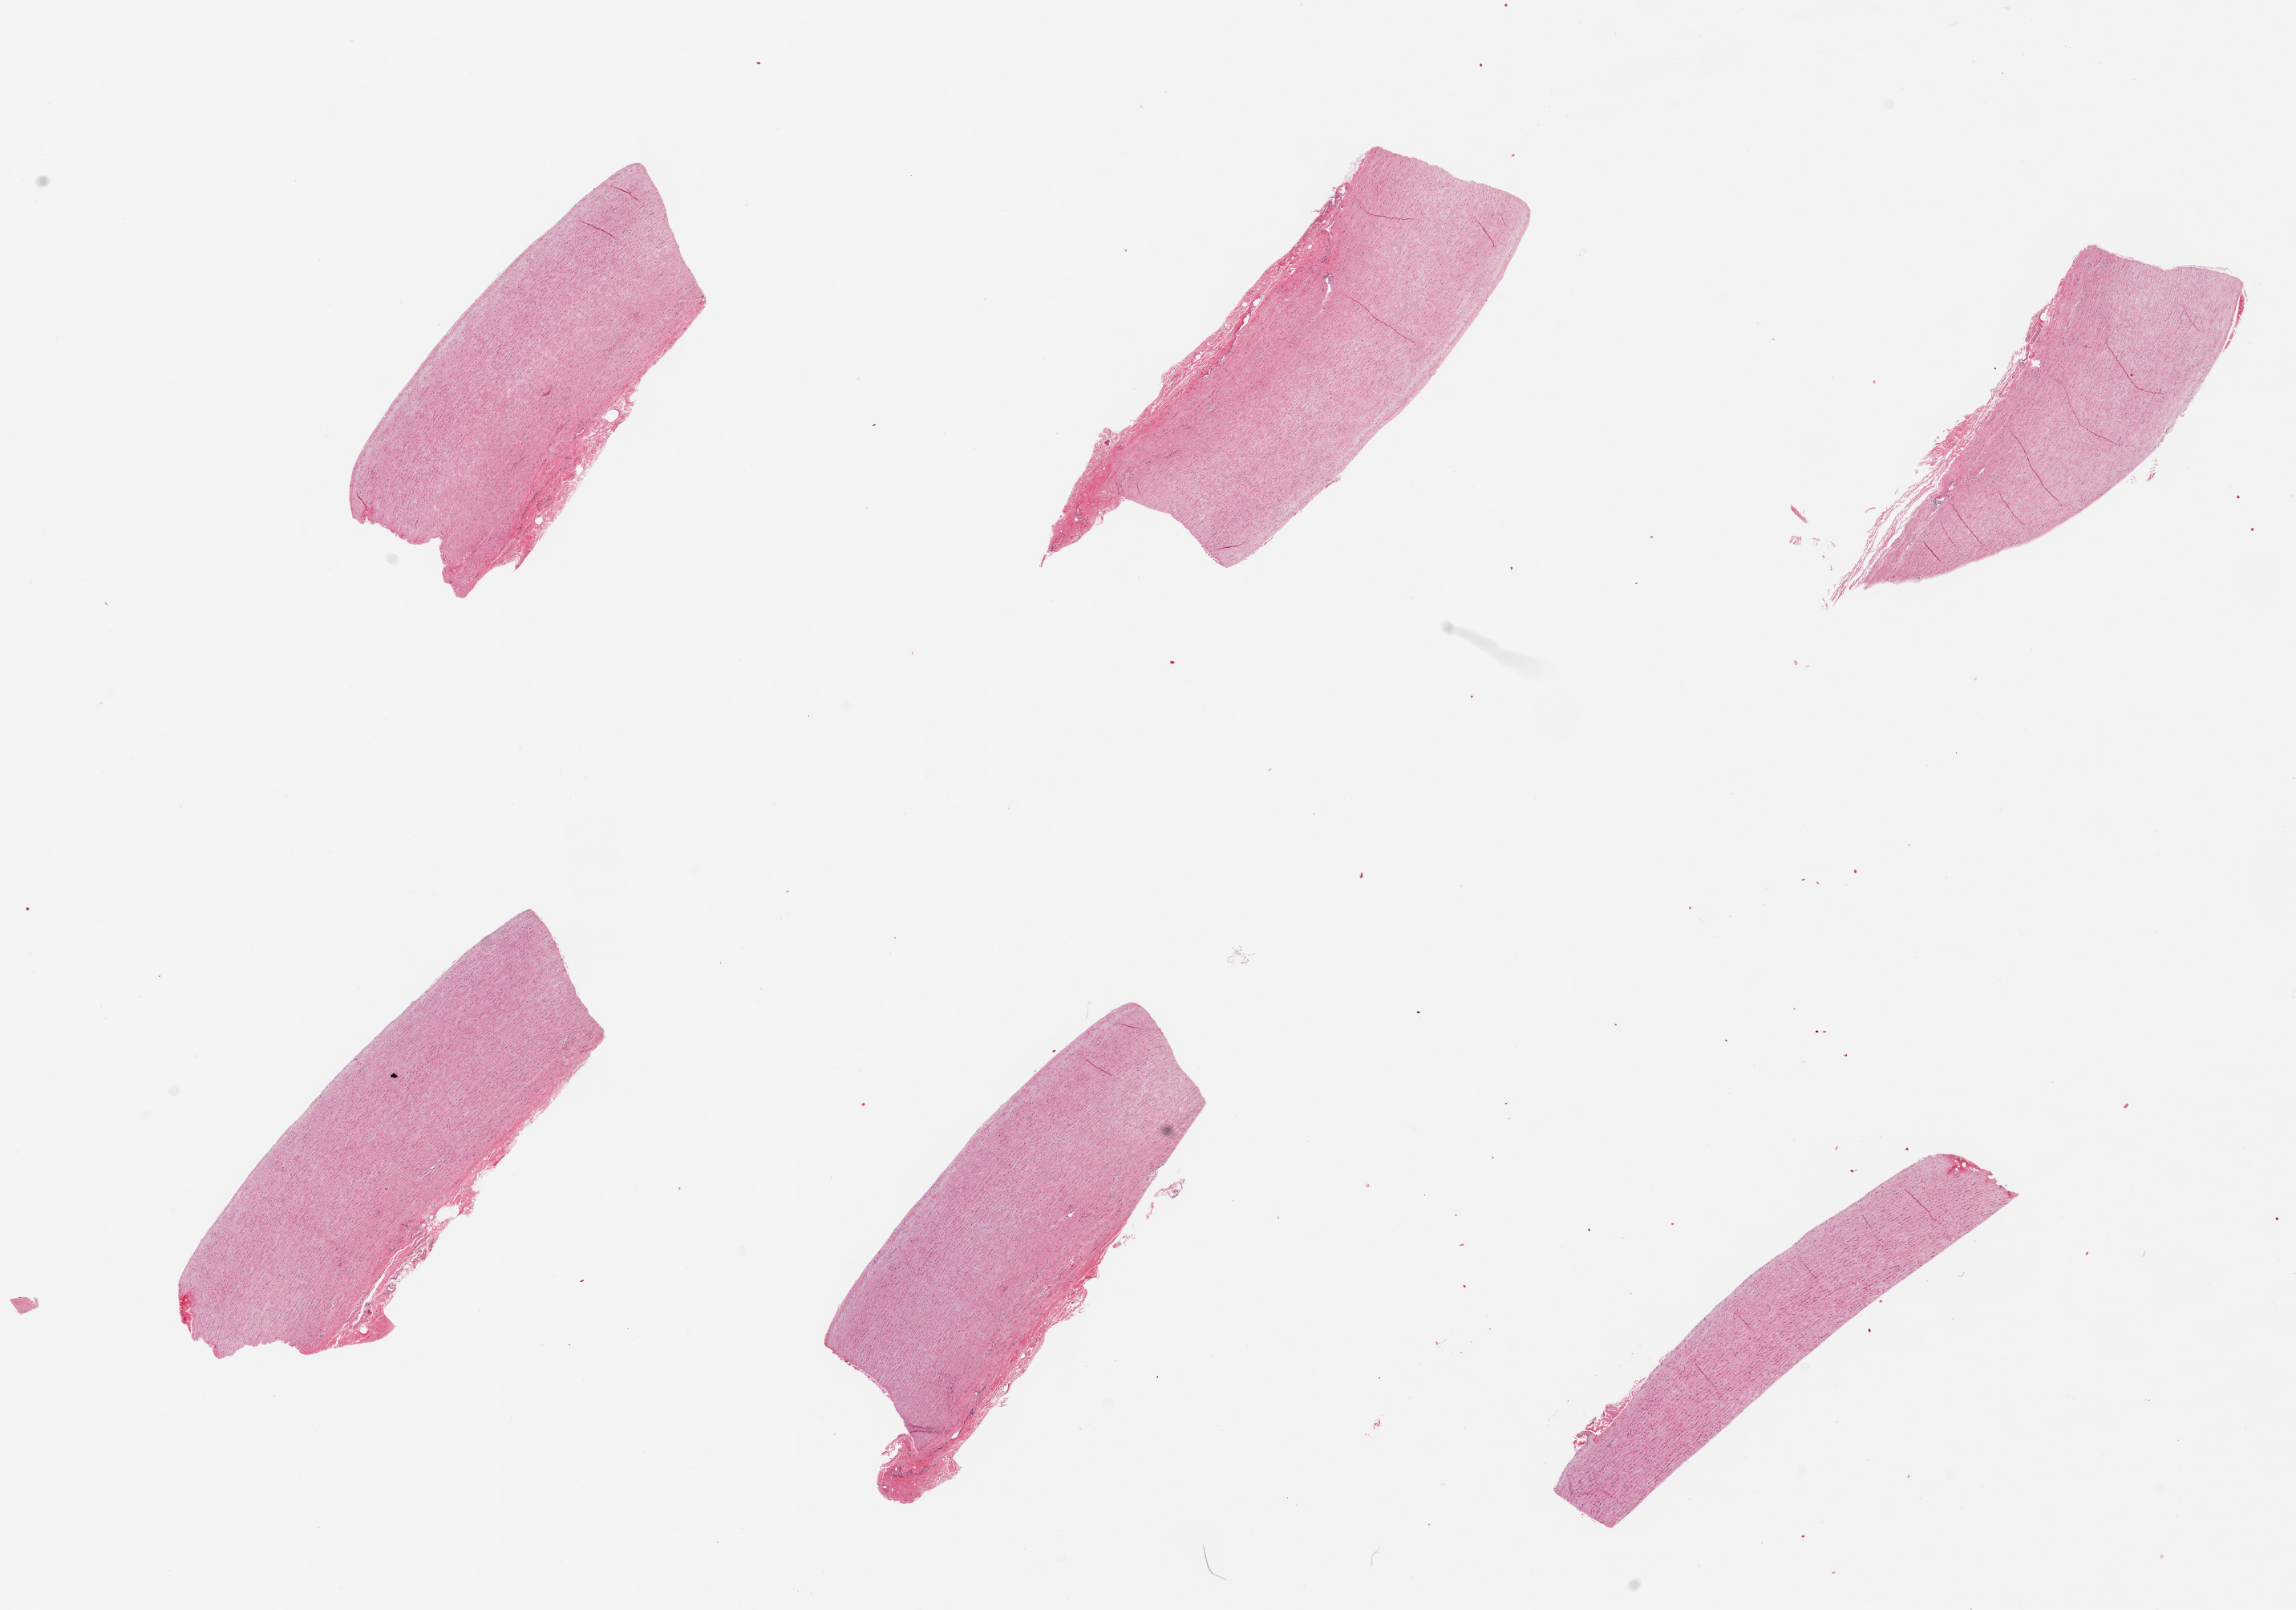
Whole-slide image, hematoxylin and eosin (H&E) stain — a low-resolution overview of the entire scanned area, about 22.6 x 15.9 mm, PAXgene-fixed paraffin-embedded (PFPE) section, target tissue: aorta, donor tissue sample. Donor: male.
Reviewer comment on this tissue sample: 6 pieces, mild atherosis.